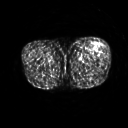
FDG PET of an extremity soft-tissue mass (from a PET/CT study), one axial slice; position 217 of 267 along the scan axis; 3.27 mm slice thickness; 128 × 128 image matrix. Patient: male, 64 years. From the clinical record (not read from this slice): histological type: extraskeletal osteosarcoma; grade: high; site of the primary tumour: thigh.
Annotated regions visible in this slice (expert contour drawn on MRI and transferred to this co-registered scan by the dataset authors):
- gross tumour volume (mass): bounding box (x1, y1, x2, y2) in pixels: (96, 44, 100, 51)